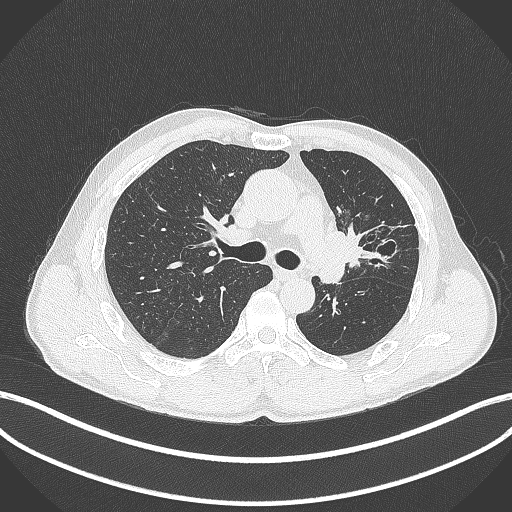
Chest CT, one axial slice. Slice 267 of 429 in the series (ordered by position). Reconstruction kernel B70f. 120 kVp. Lung window (W 1500 / L -600 HU). 1 mm slice thickness. 512 × 512 image matrix, field of view 400 × 400 mm. Male patient, age 57 years. From the clinical record (not read from this slice): clinical TNM (as recorded): T2b N0 M0.
Annotated regions visible in this slice (bounding box drawn by a radiologist):
- lung tumour (recorded histology: squamous cell carcinoma): box from (x=318, y=225) to (x=364, y=266) px